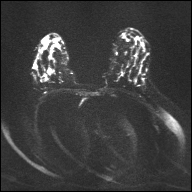
Breast MRI, one axial slice; position 22 of 32 along the scan axis; diffusion-weighted series; image 2 of 4 stored at this slice position (different b-values; order by instance number); 1.5 T; 4 mm slice thickness; 192 × 192 image matrix, field of view 360 × 360 mm. Female patient.
Structures marked on this image (manually delineated by an expert):
- tumour on diffusion-weighted imaging: box from (x=33, y=64) to (x=52, y=82) px